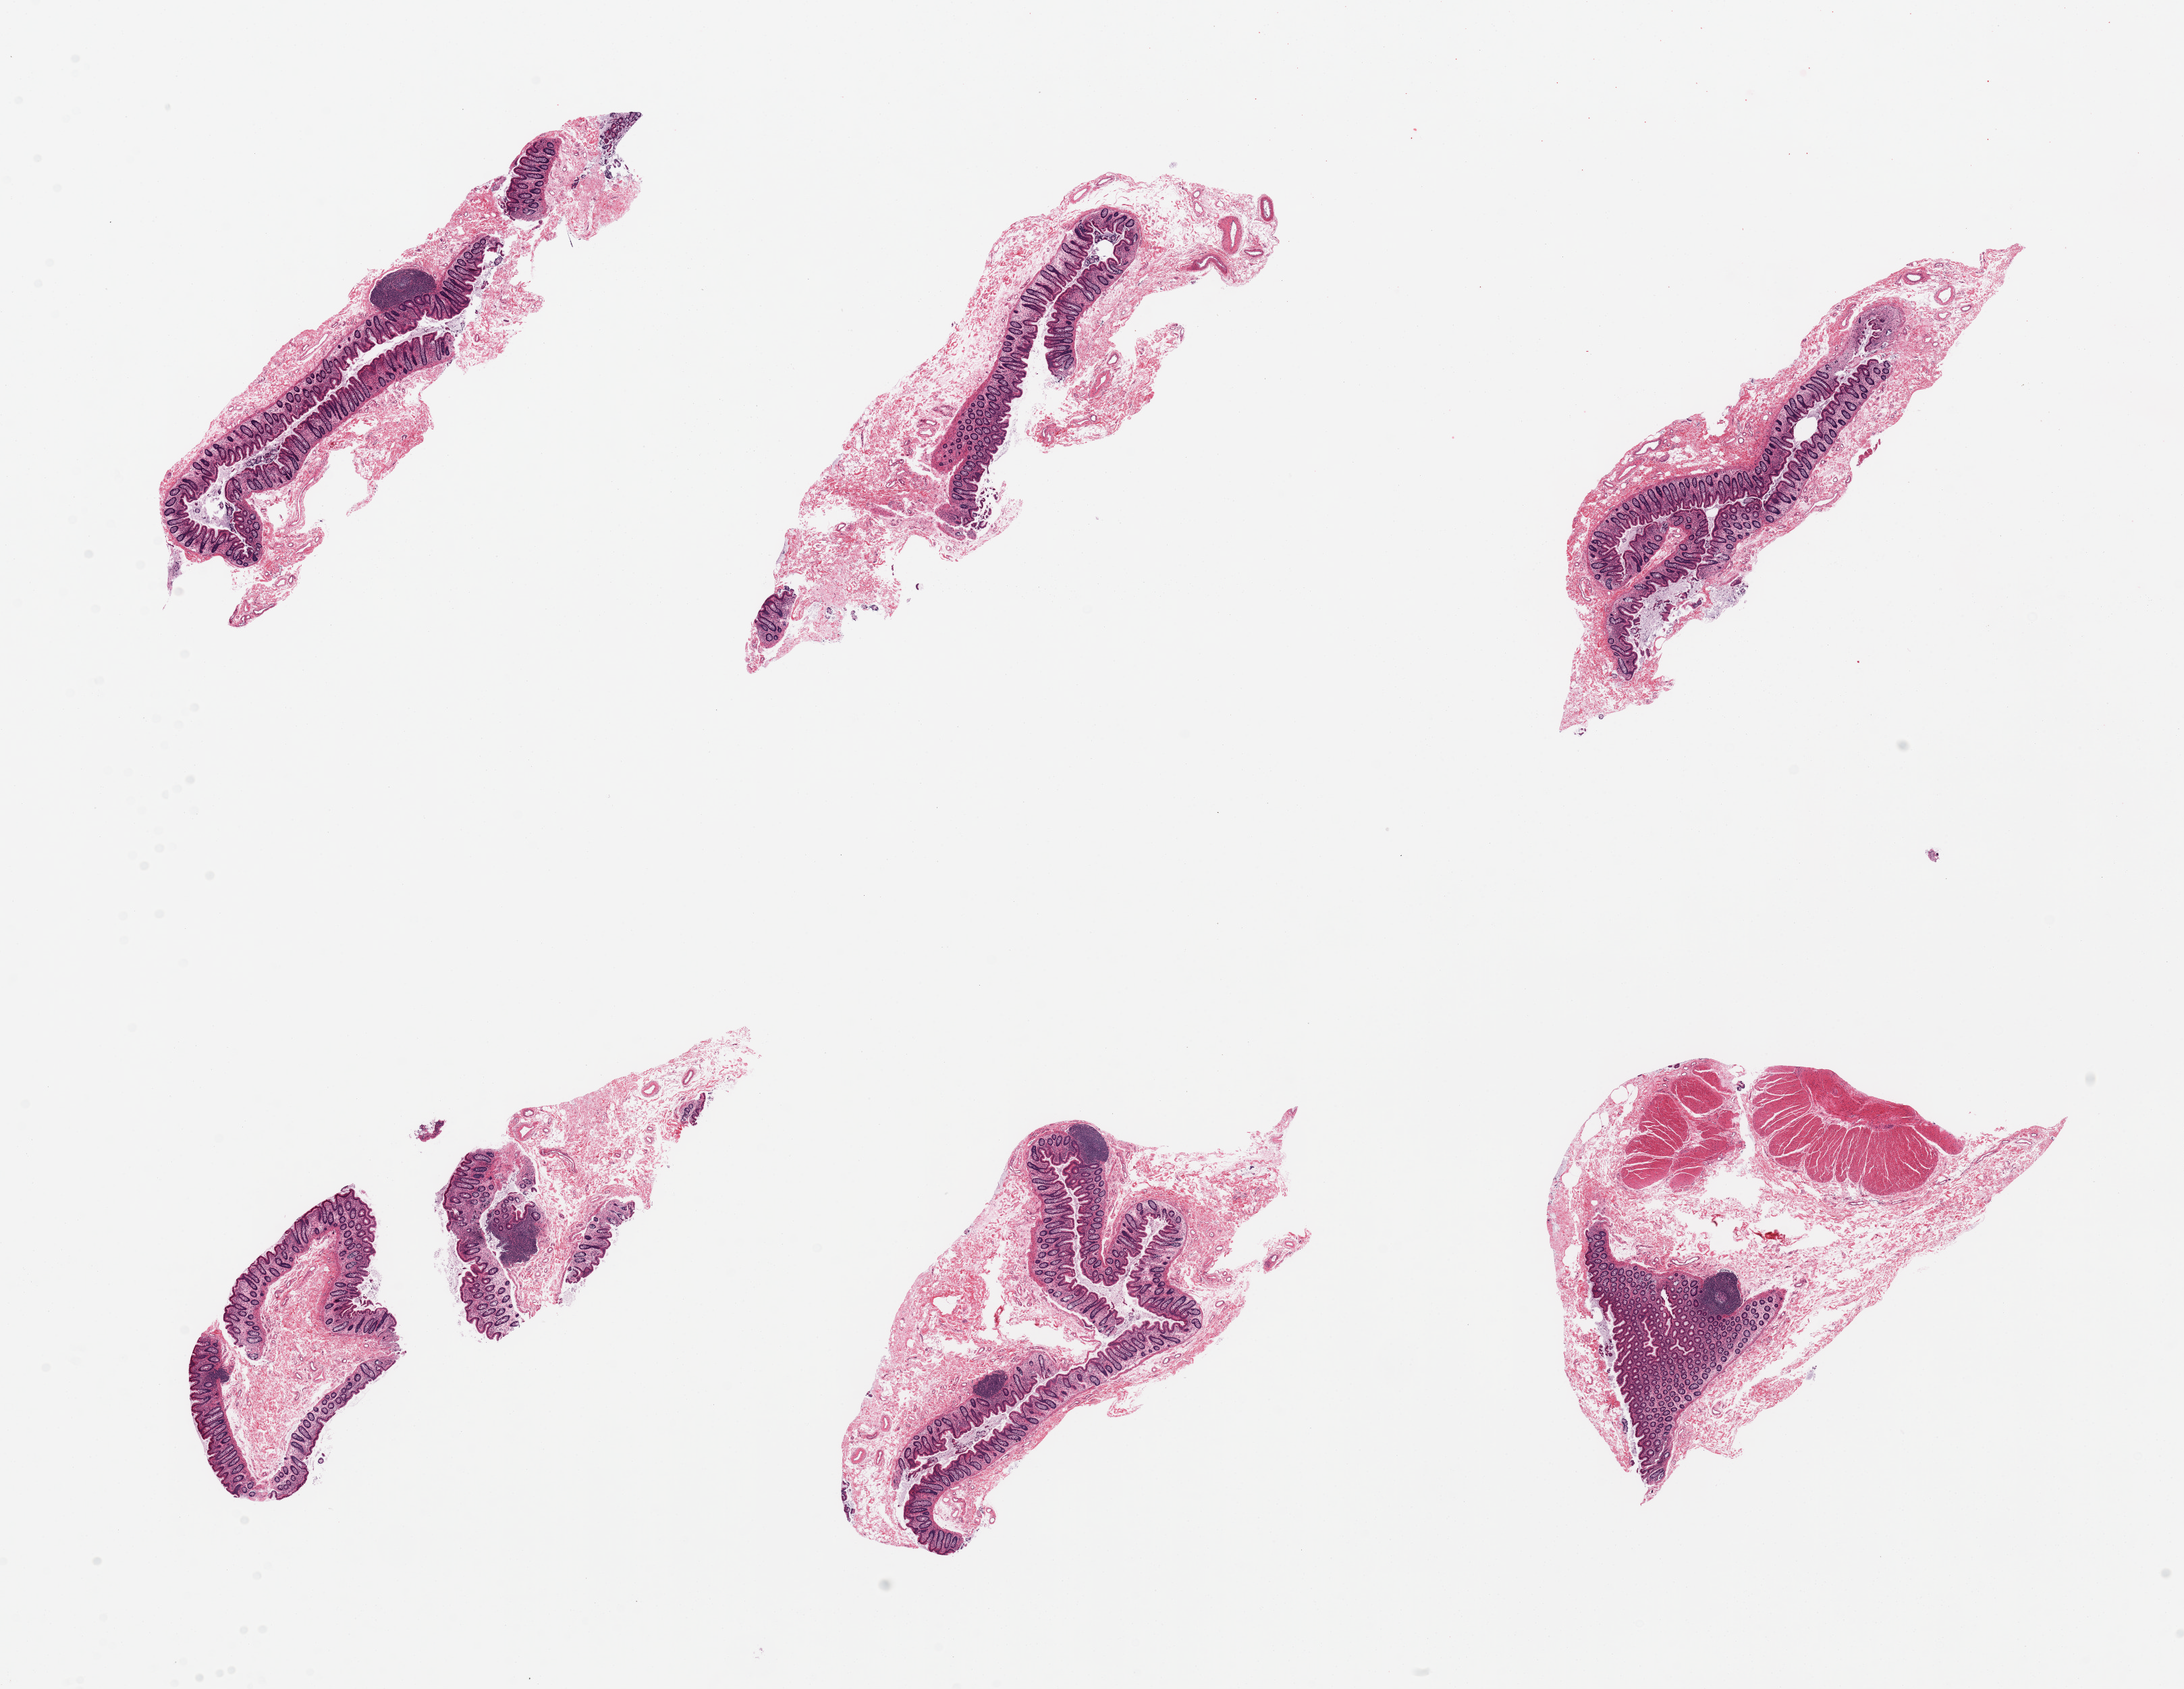
Digitized H&E-stained section, brightfield — whole scanned area (about 25.6 x 19.8 mm, from a 20x scan) shown as a low-resolution overview. PAXgene-fixed, paraffin-embedded tissue. Section of transverse colon (target tissue). Tissue donor sample.
Review note (as recorded): 6 pieces, well preserved mucosa.